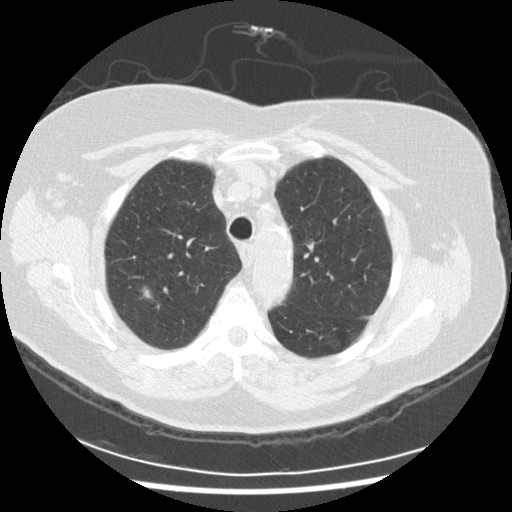
Low-dose screening chest CT, axial slice; third annual screen; lung window (W 1500 / L -600 HU); standard (soft-tissue) reconstruction kernel (STANDARD); 120 kVp. Female participant, aged 72 years at enrolment.
- Lesion marked by an expert reader, bounding box (x1, y1, x2, y2) in pixels: (127, 280, 159, 307).
- The exam's reader record, not a measurement of the box and not confirmed to be the same lesion: non-calcified nodule or mass ≥4 mm, right upper lobe, 9 × 8 mm, poorly defined margins, ground glass attenuation, pre-existing on the prior screen: no.
- Participant outcome: lung cancer diagnosed 121 days after this screen — squamous cell carcinoma, NOS, right upper lobe, poorly differentiated (G3), stage IIIA (AJCC 6th edition), 22 mm at pathology.